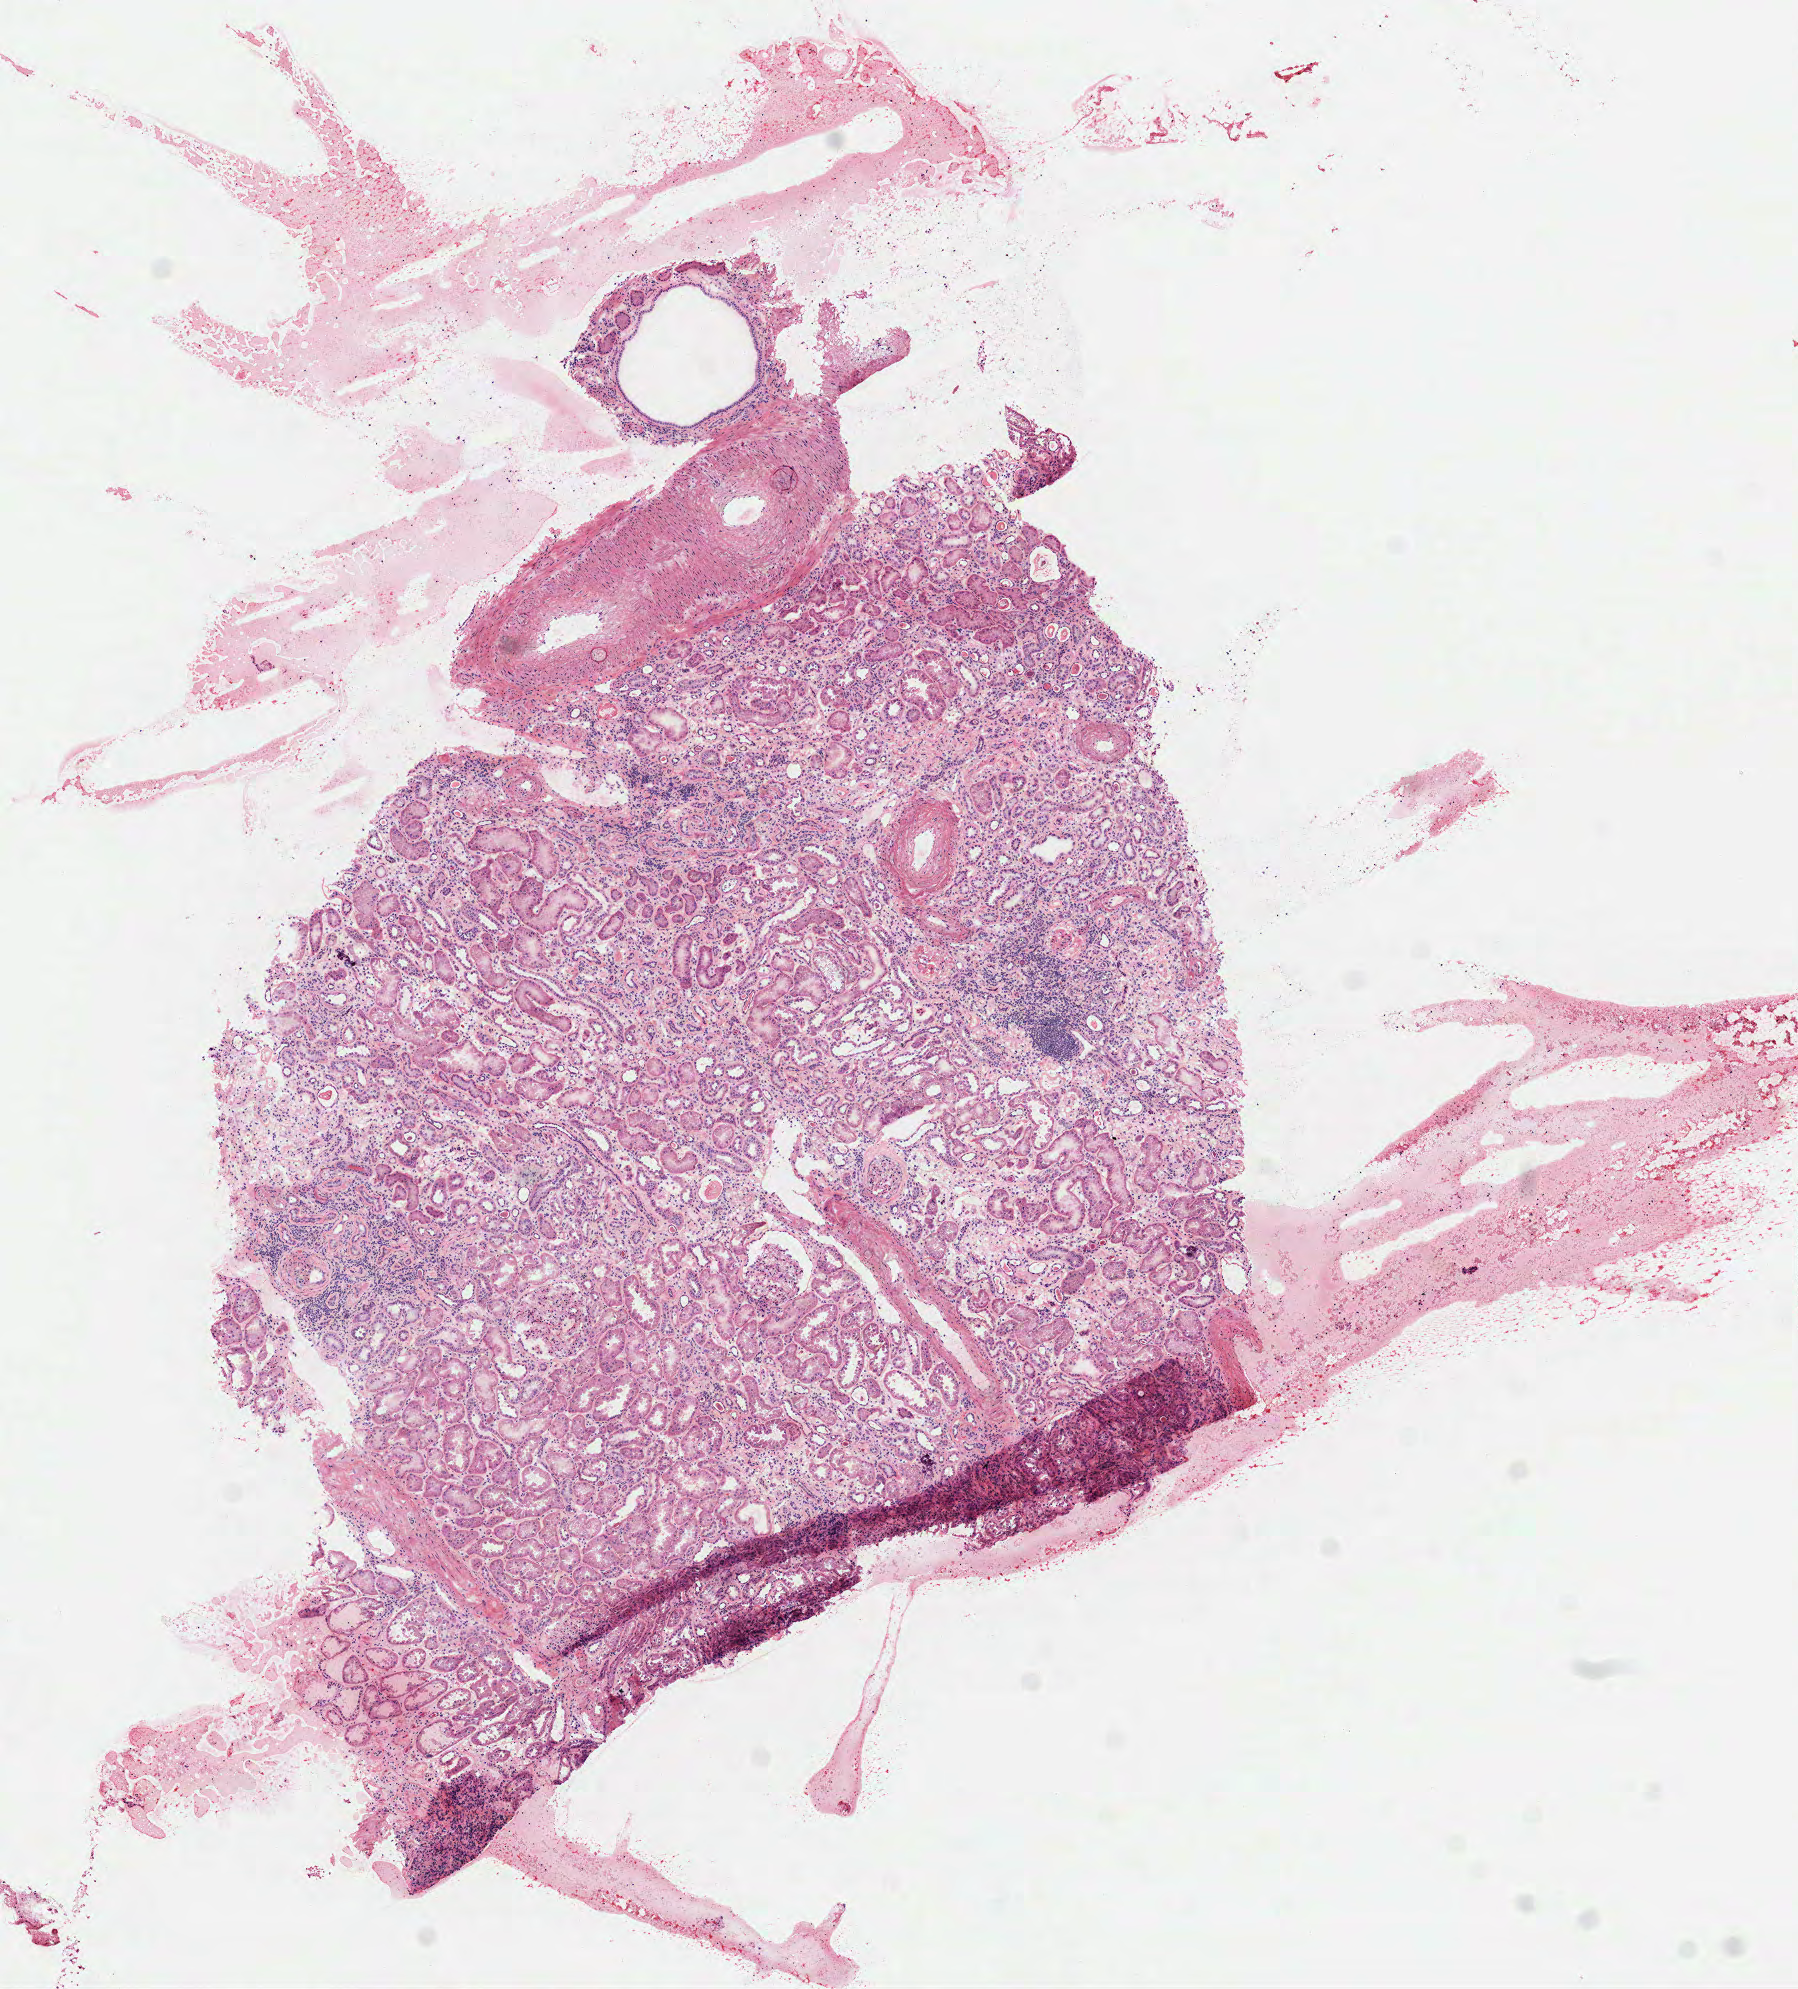
Digitized H&E-stained tissue section (whole slide), shown as a low-resolution overview of the whole scanned area (about 7.3 x 8.0 mm, acquisition: 40x scan); frozen section from the top of the tissue portion; sample: solid tissue normal (non-tumour tissue), kidney. Patient: male, age at initial diagnosis 78 years.
* this section: solid tissue normal sample (biorepository sample class)
* patient diagnosis: Papillary adenocarcinoma, NOS